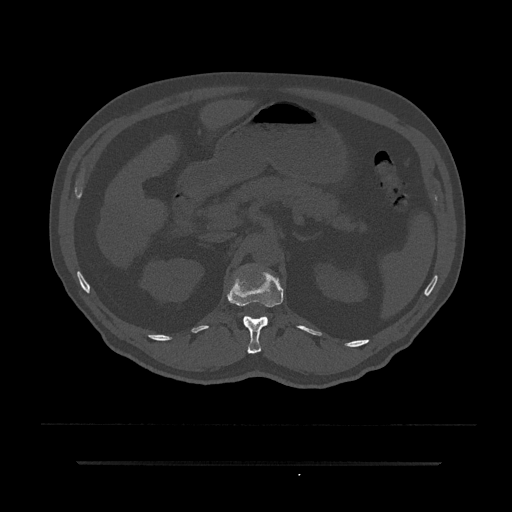
CT including the spine, one axial slice; position 189 of 797 along the scan axis; bone window (W 1800 / L 400 HU); 512 × 512 image matrix. Male patient, age 59 years. From the clinical record (not read from this slice): primary cancer: bile ducts; vertebrae with lytic lesions (as recorded): T10.
Outlined on this slice (semi-automatic segmentation, software-assisted and operator-edited):
- T12 vertebra: bounding box <227,269,283,354> (left, top, right, bottom; pixels)